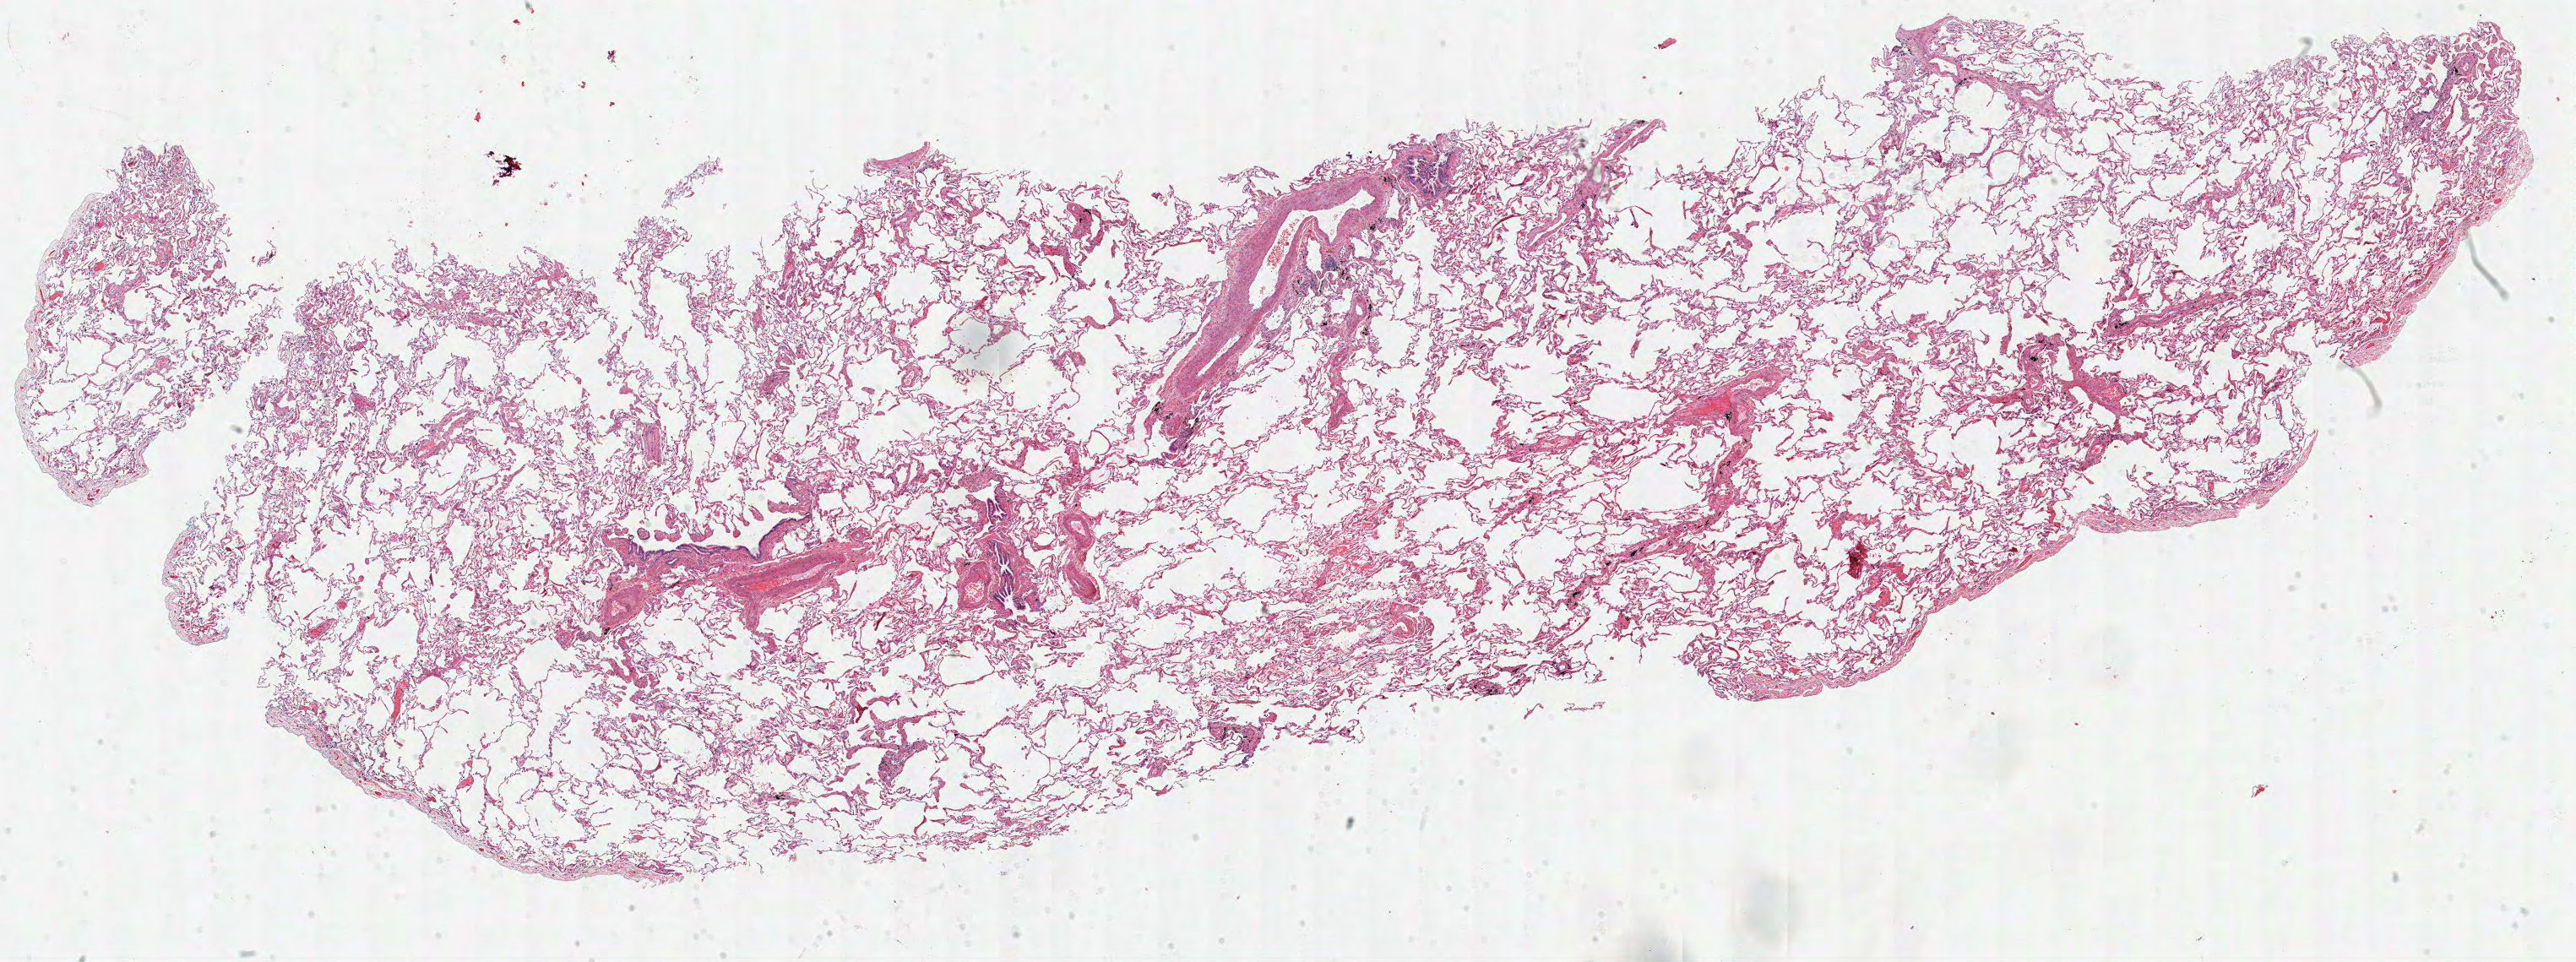
Digitized H&E tissue section (whole slide), low-resolution overview of the scanned area, about 24.0 x 9.0 mm (slide scanned at 40x); frozen section from the top of the tissue portion; solid tissue normal (non-tumour tissue) sample from the lung. Female patient; age at initial diagnosis 60 years.
* this section: solid tissue normal (non-tumour) sample from the same patient
* patient diagnosis: Adenocarcinoma, NOS (upper lobe, lung)